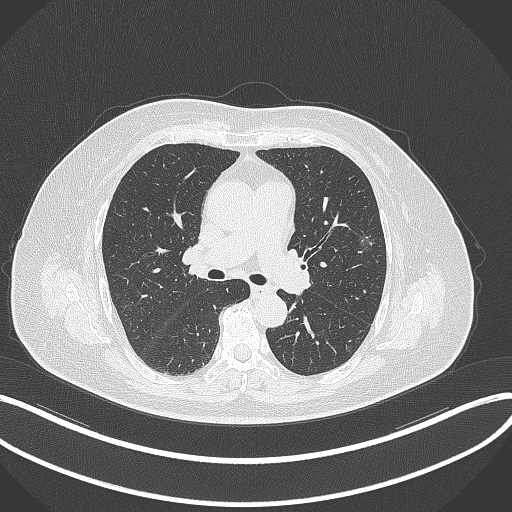
Chest CT, one axial slice; position 216 of 315 along the scan axis; 120 kVp; lung window (W 1500 / L -600 HU); 512 × 512 image matrix, field of view 400 × 400 mm. Female patient, age 76 years. From the clinical record (not read from this slice): clinical TNM (as recorded): T1b N0 M0.
Structures marked on this image (rectangle marked by the reading radiologist):
- lung tumour (recorded histology: adenocarcinoma): bounding box <351,226,375,255> (left, top, right, bottom; pixels)